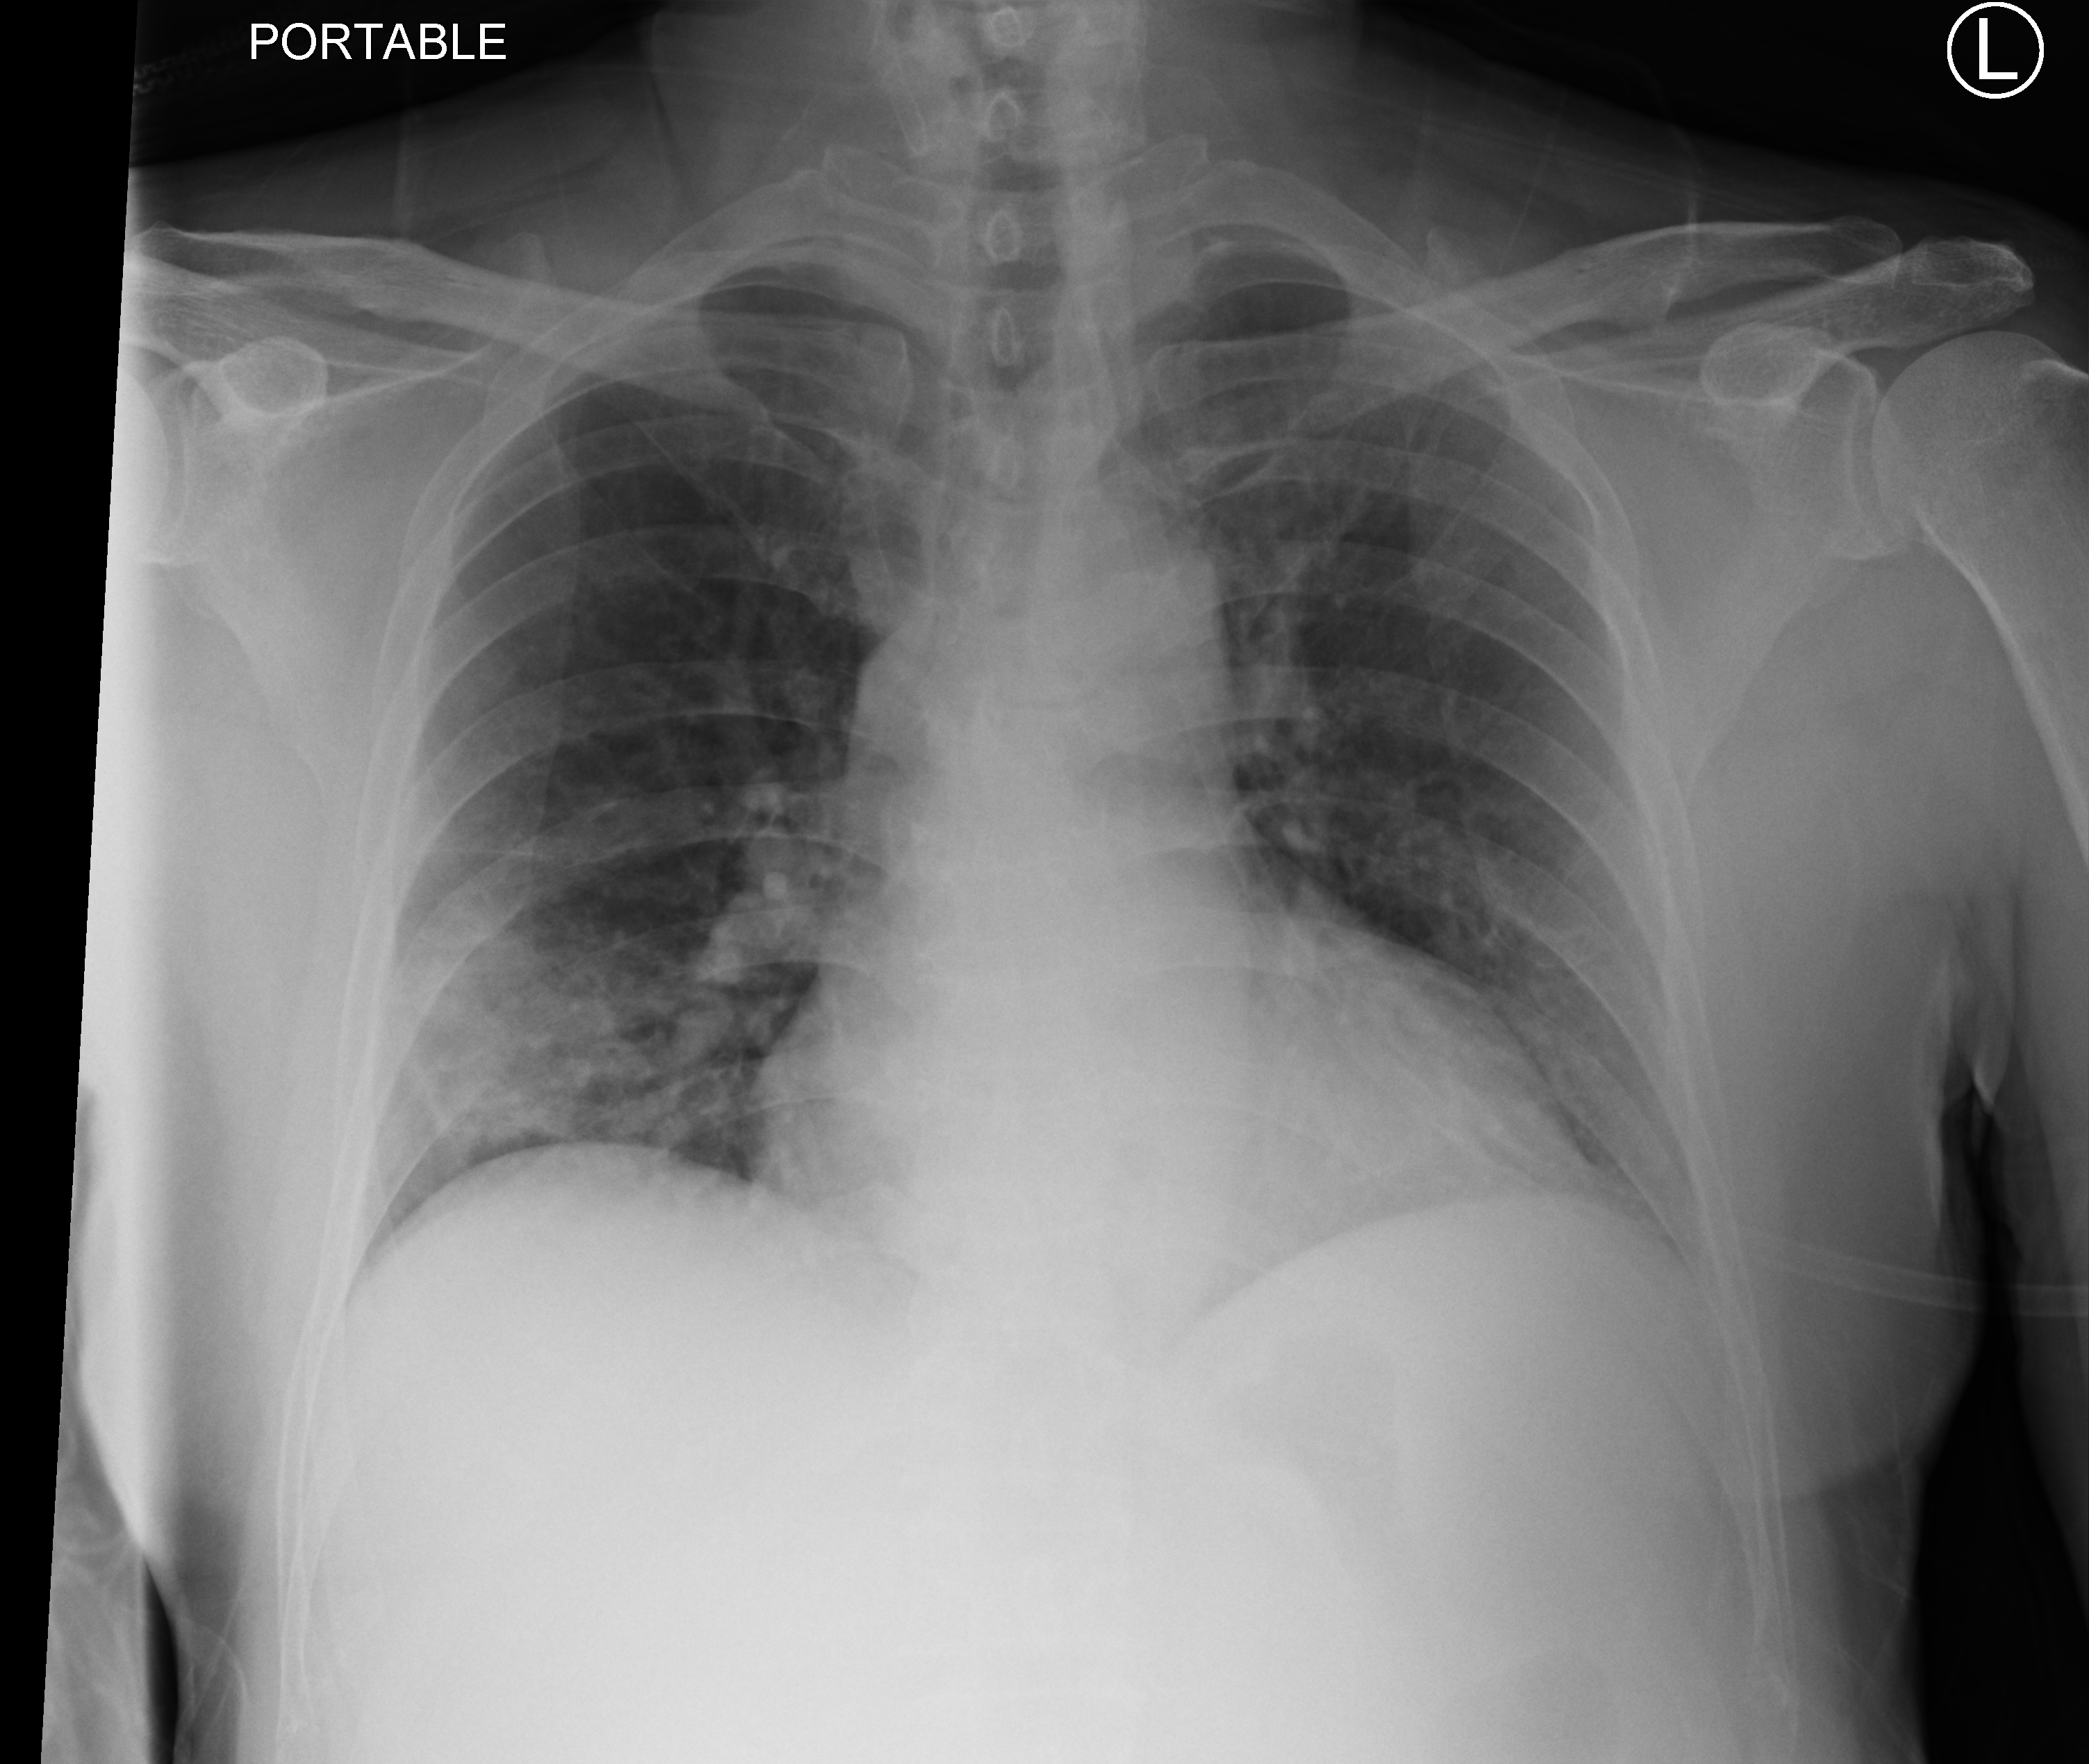
Bedside chest radiograph (computed radiography). Male patient hospitalised with COVID-19, age 60–74 years.
Admission-level facts for this patient (not findings on this image; timing relative to this image not recorded):
- admitted to intensive care during this hospital stay: no
- smoking status (admission record): never